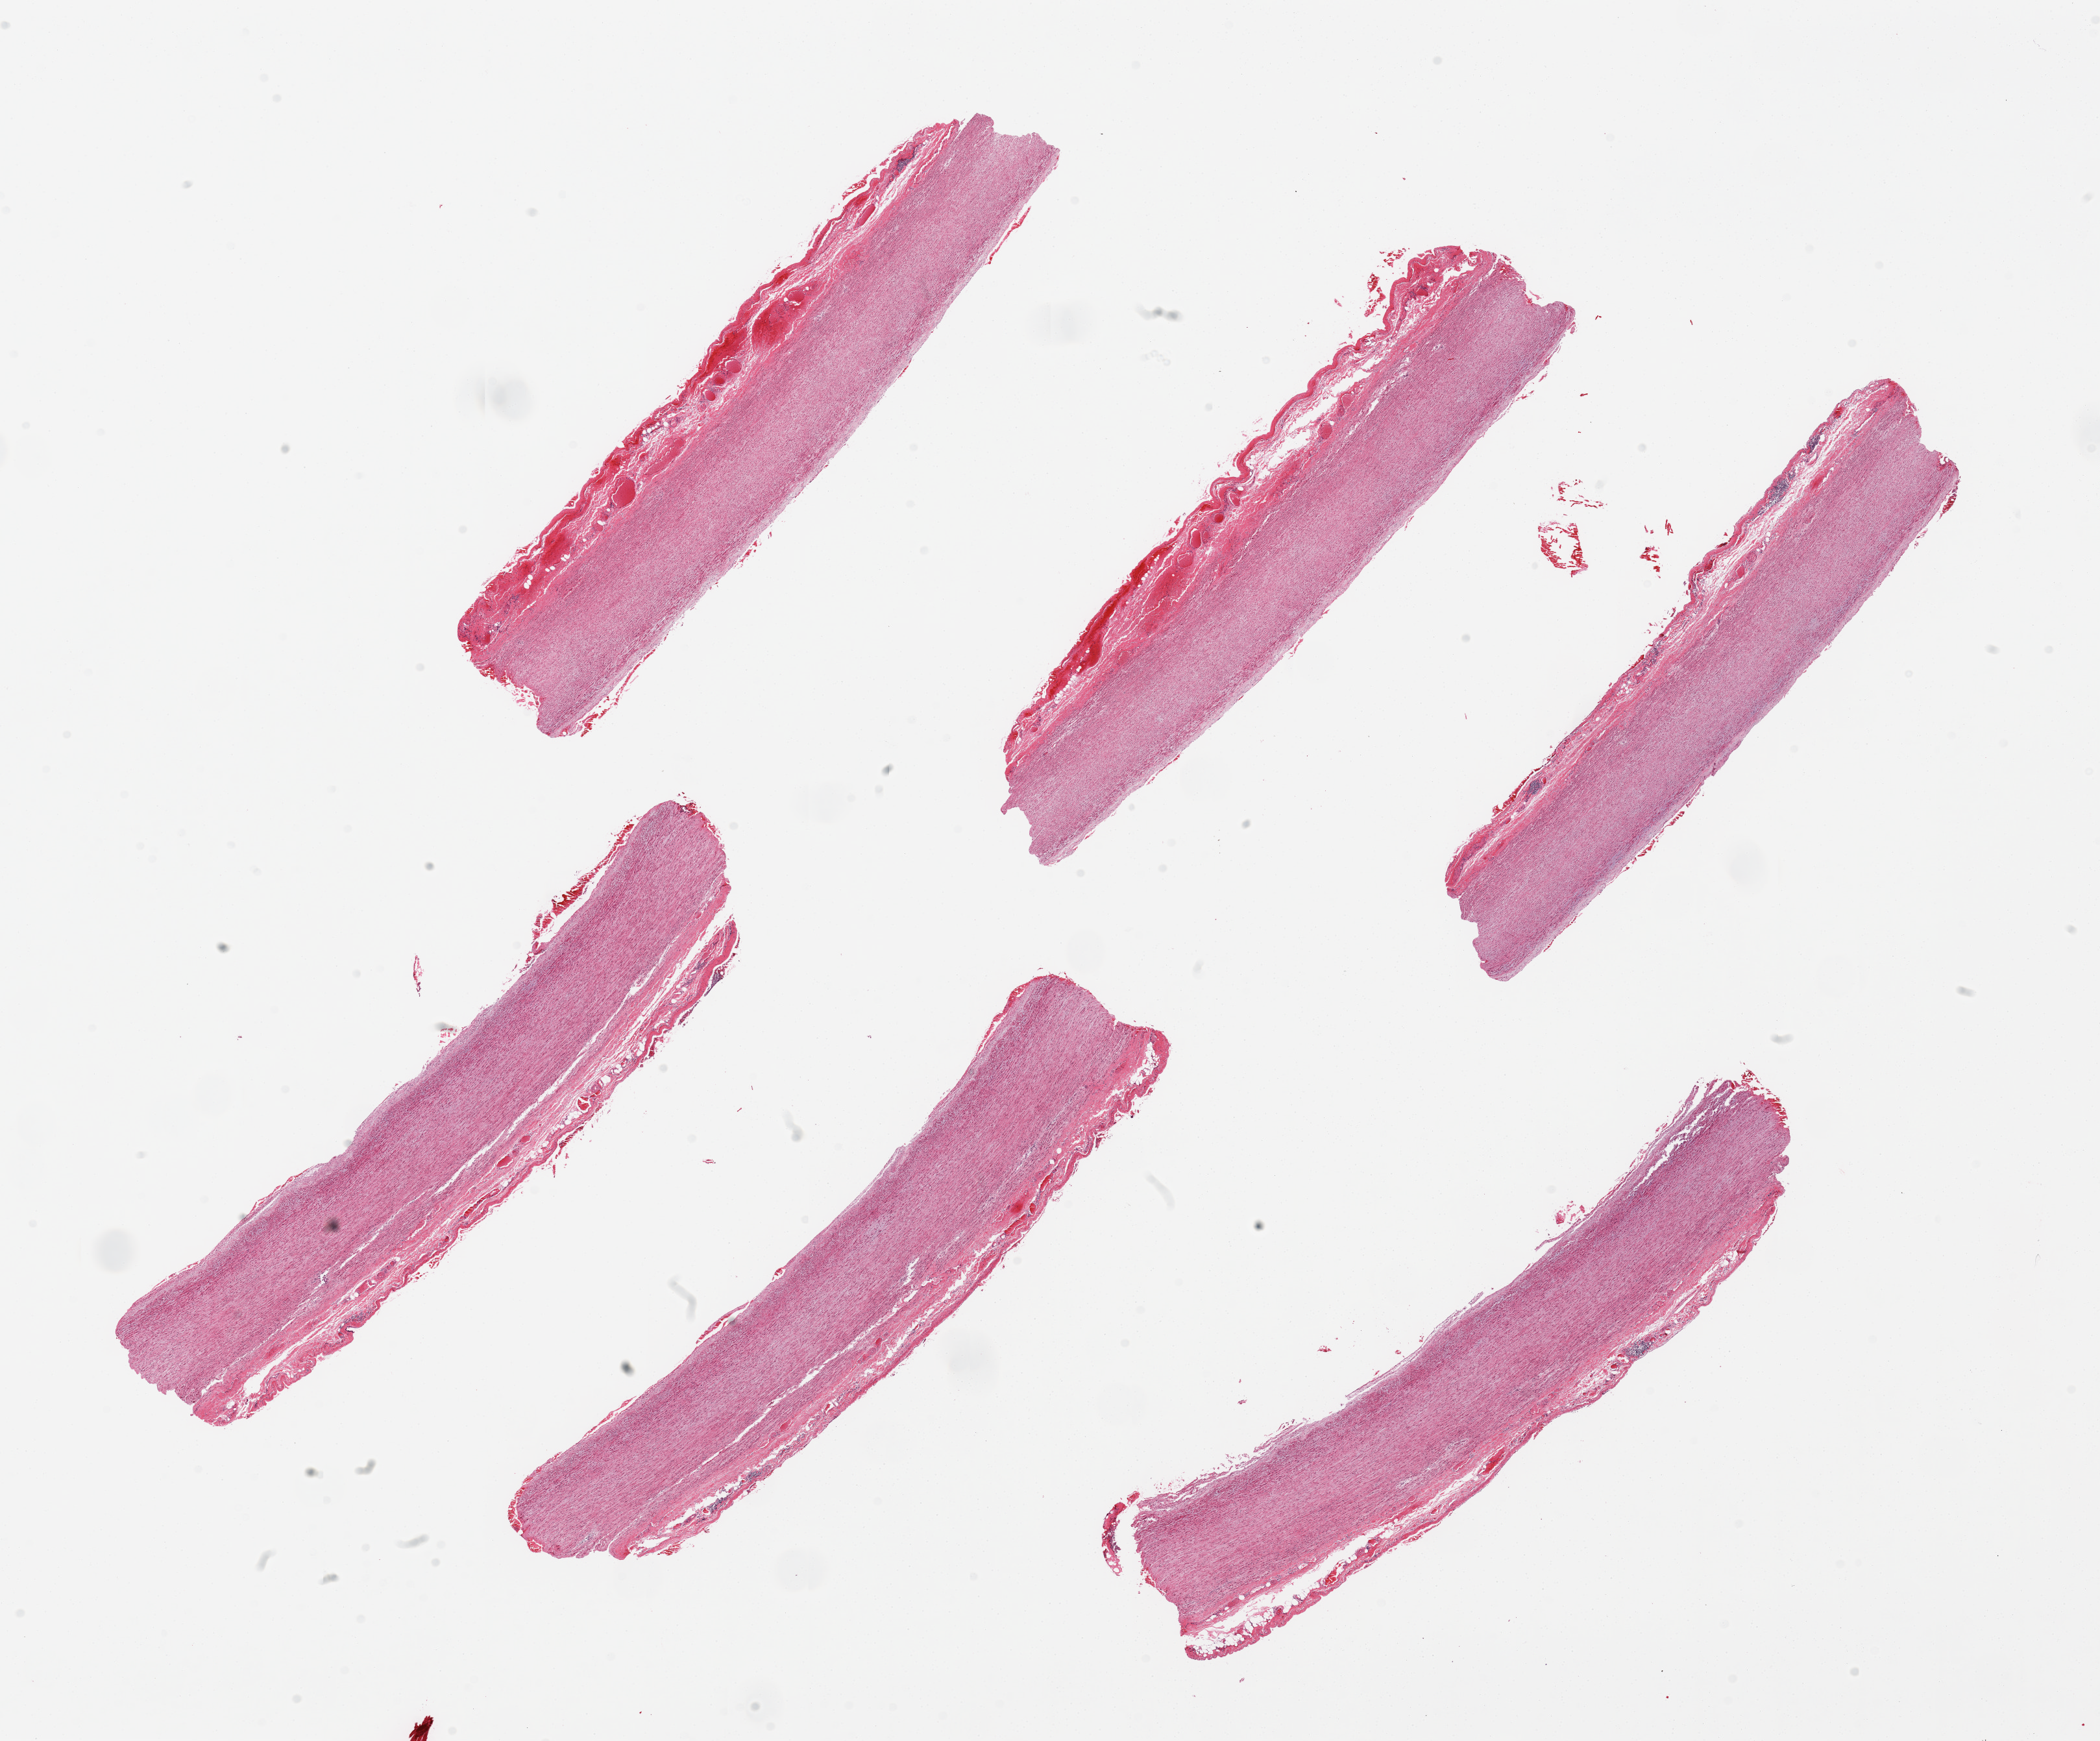
Digitized haematoxylin and eosin-stained section, brightfield, shown as a low-resolution overview of the whole scanned area (about 25.6 x 21.2 mm, acquisition: 20x scan); PAXgene-fixed paraffin-embedded (PFPE) section; target tissue: aorta; donor tissue sample. Female donor.
- review note (as recorded): 6 pieces, congested serosa up to ~0.5mm